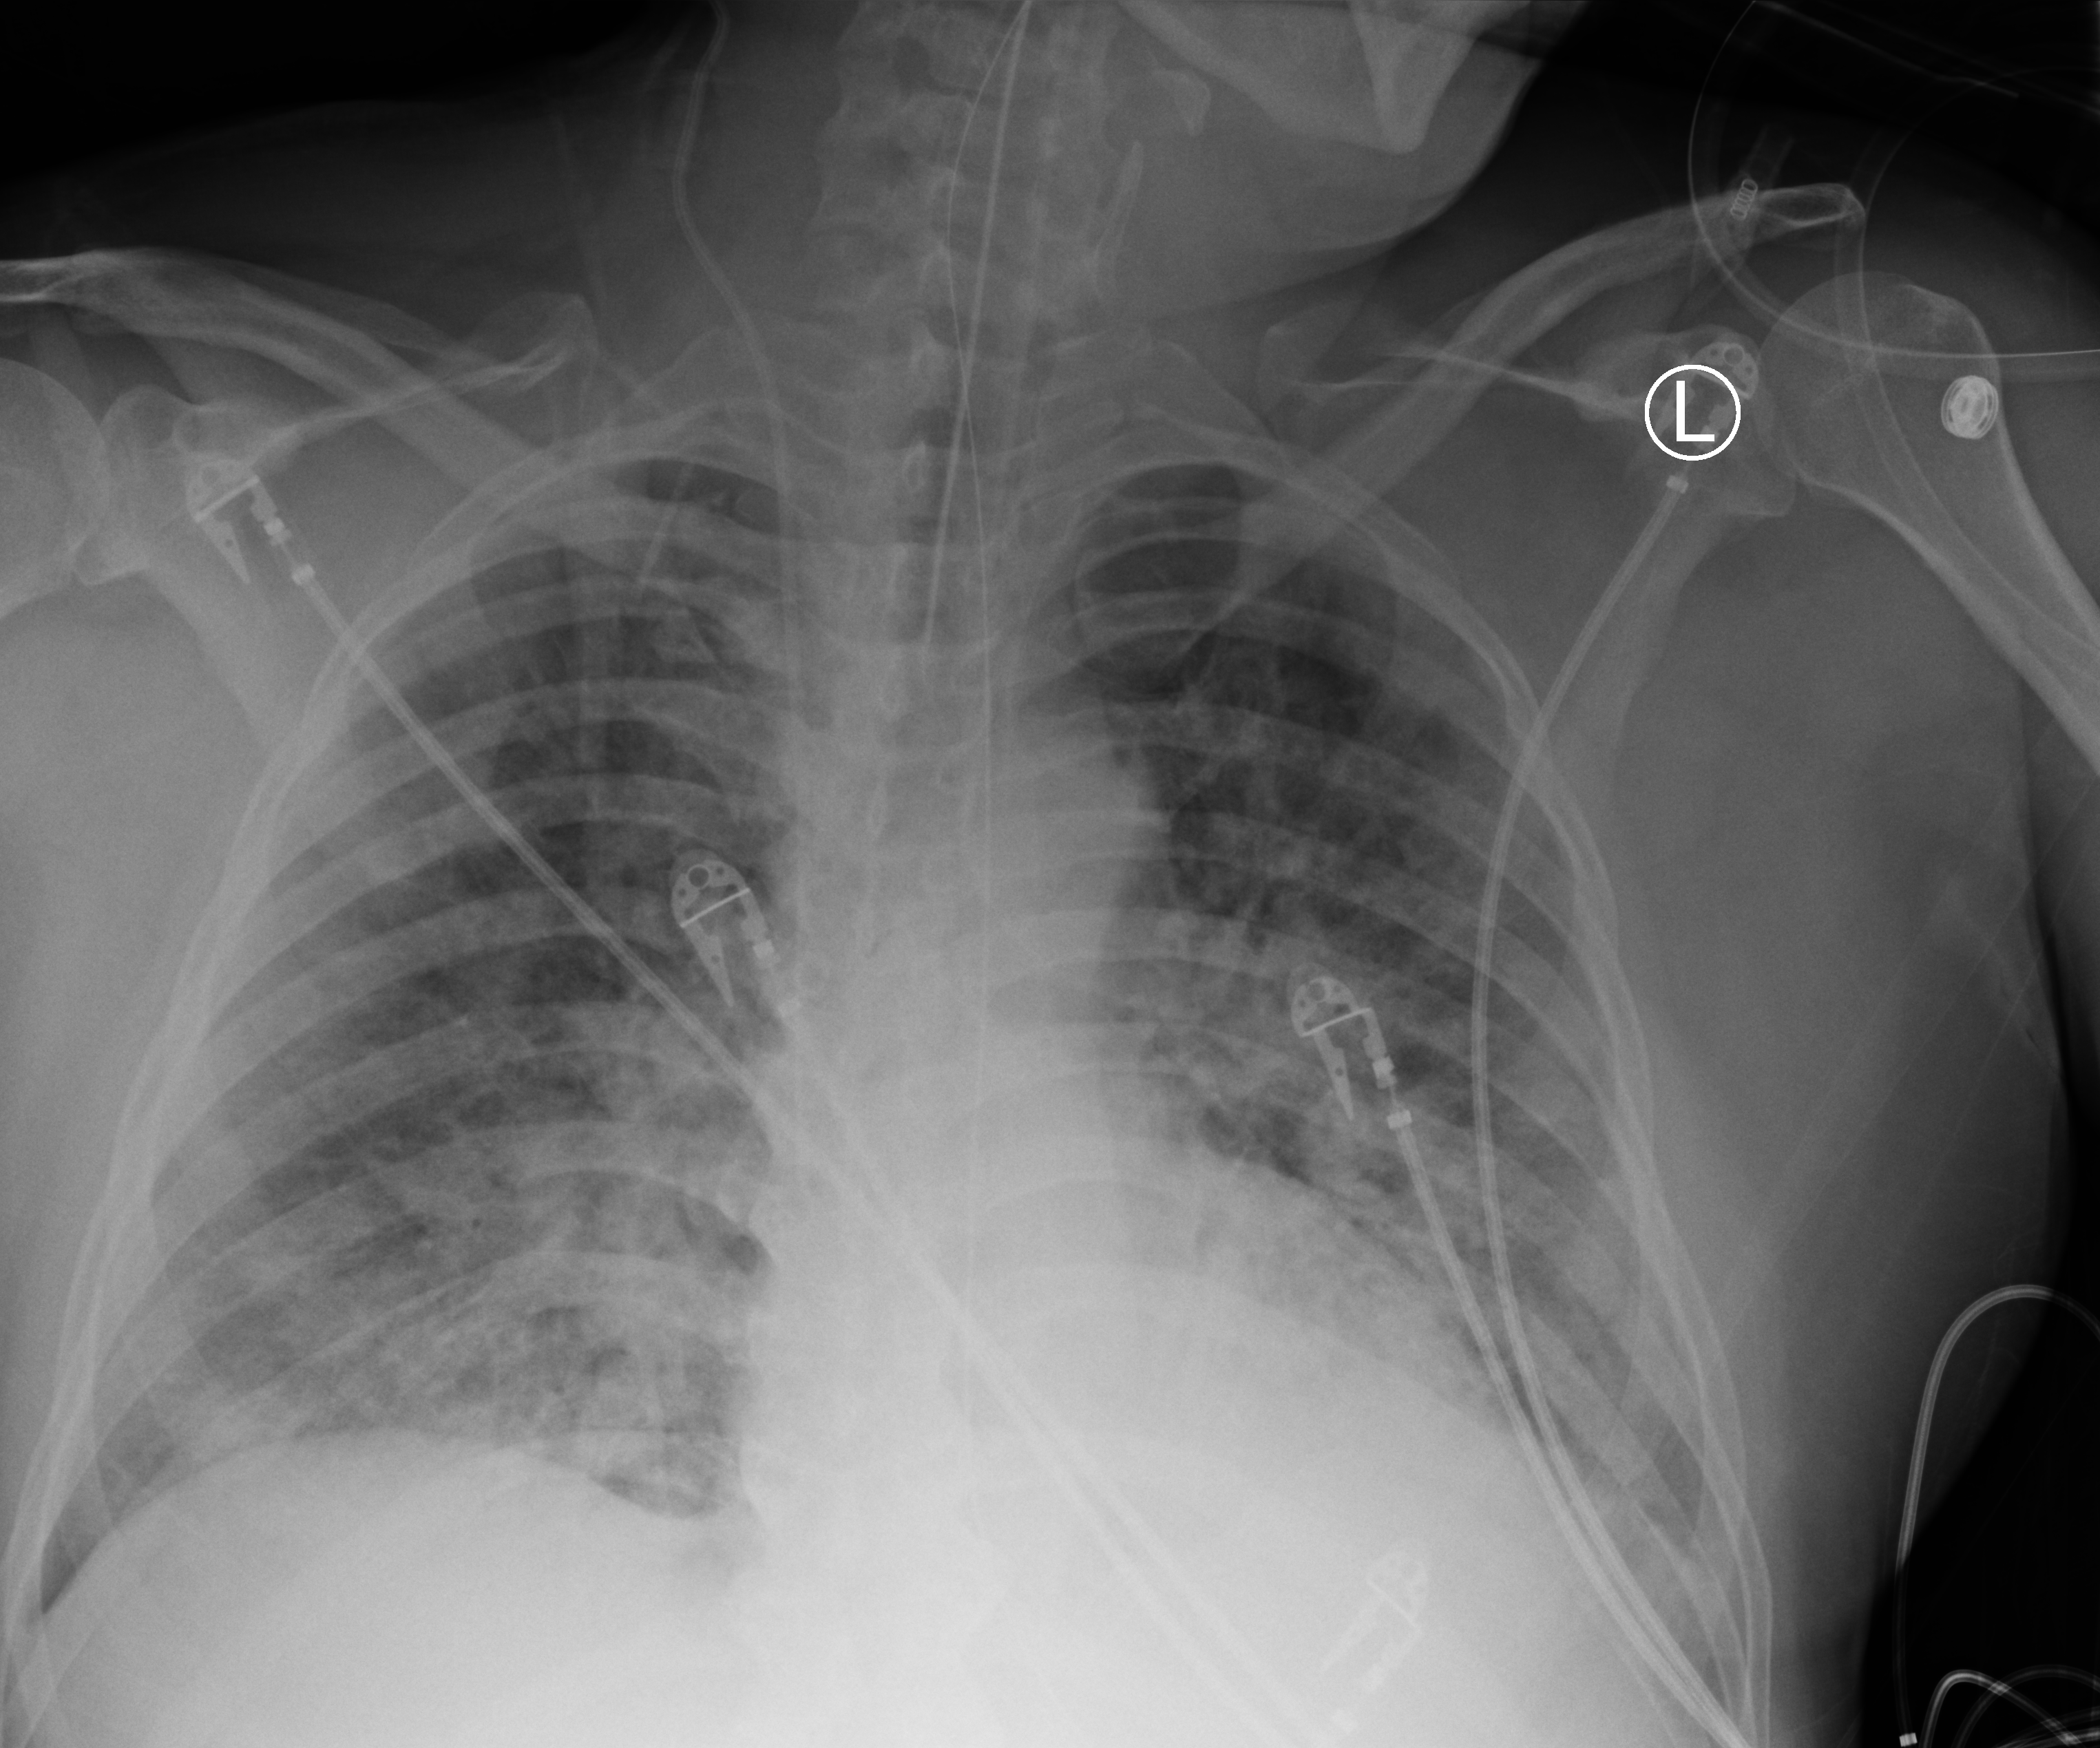
Chest X-ray (portable); anteroposterior (AP) projection. Patient hospitalised with COVID-19; male, aged 18–59 years.
From the hospital-stay record, not from the radiograph (when in the stay this image was taken is not recorded): hypertension (admission record): yes.